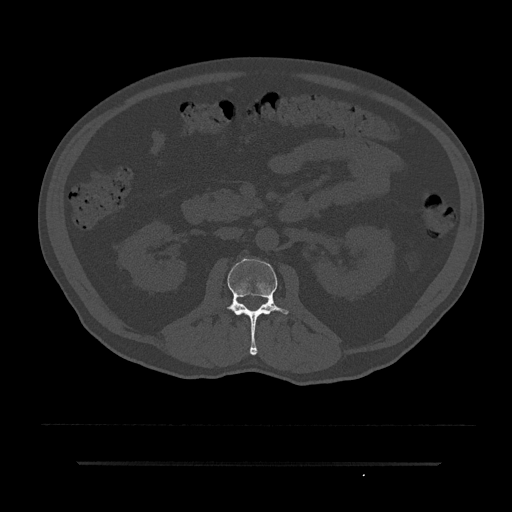
CT including the spine, one axial slice. Slice 73 of 797 in the series (ordered by position). Reconstruction kernel Br40s/3. 120 kVp. Bone window (W 1800 / L 400 HU). 0.5 mm slice thickness. 512 × 512 image matrix. Male patient, age 59 years. From the clinical record (not read from this slice): primary cancer: bile ducts; vertebrae with lytic lesions (as recorded): T10.
Outlined on this slice (semi-automatic segmentation, software-assisted and operator-edited):
- L2 vertebra: bounding box <226,259,289,355> (left, top, right, bottom; pixels)